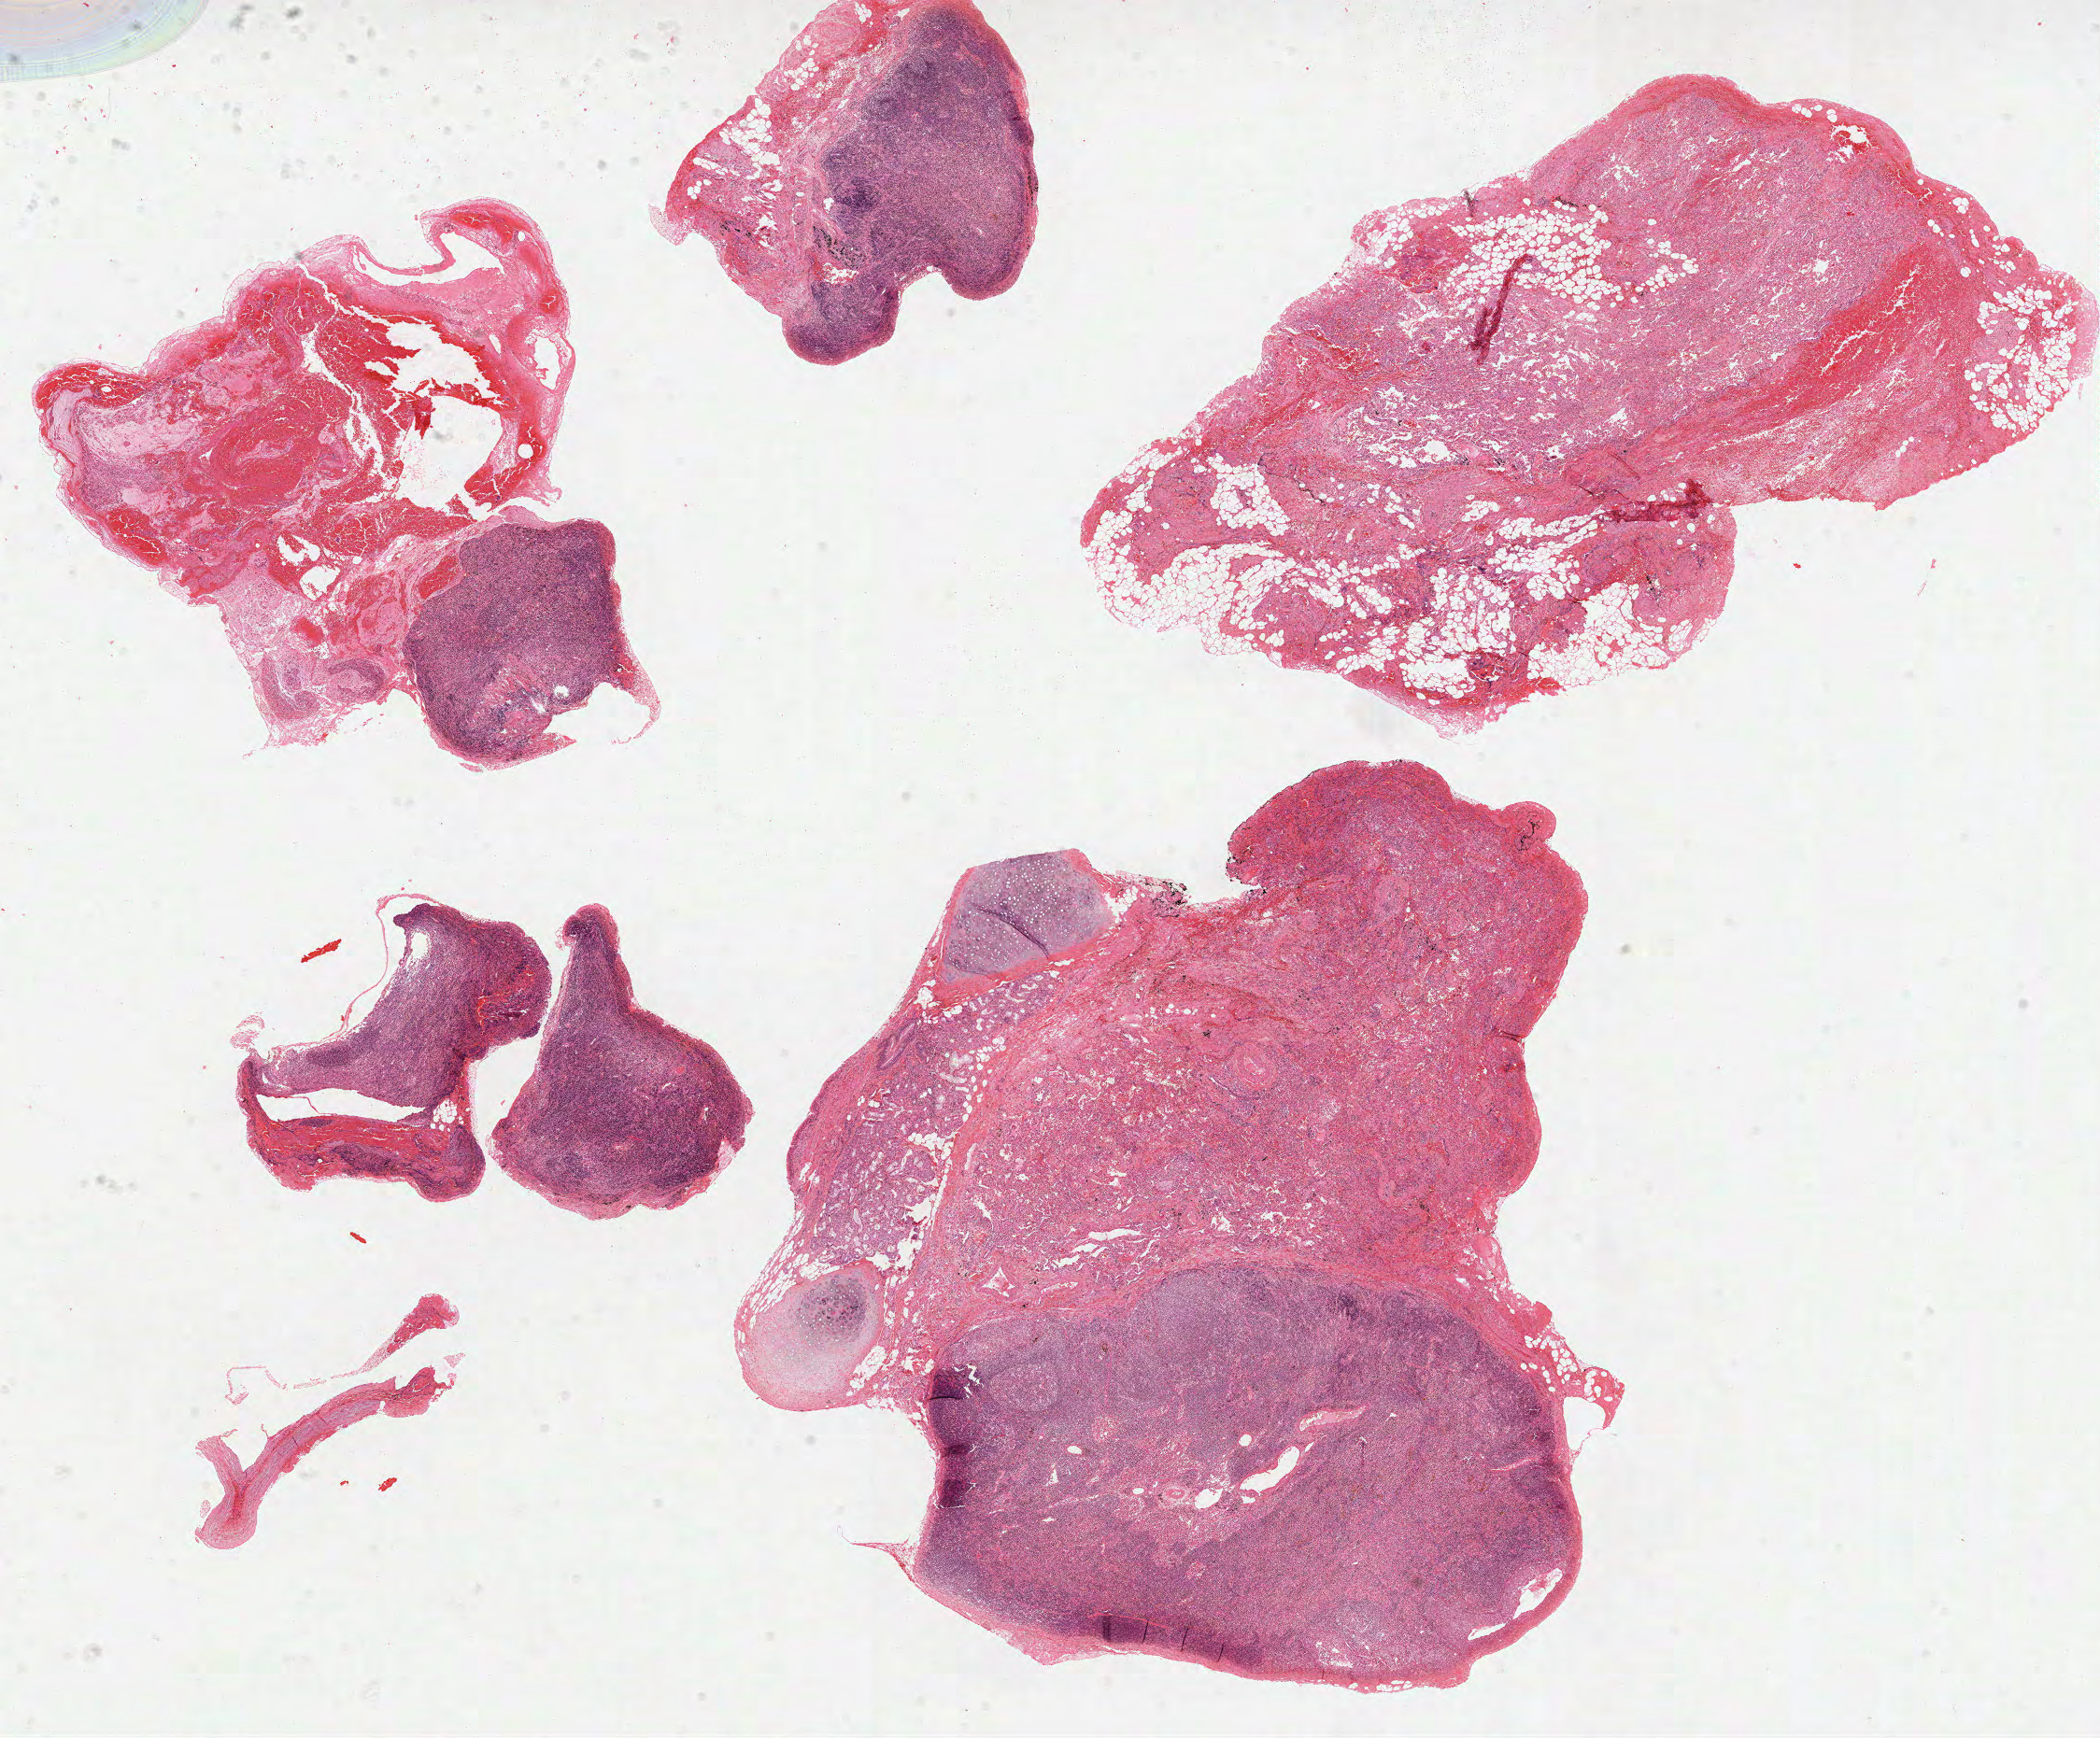
Whole-slide histology image, H&E-stained — whole scanned area (about 18.1 x 15.0 mm, acquisition: 40x scan) shown as a low-resolution overview, FFPE section, primary tumour sample from the lung. Patient: female, age at initial diagnosis 66 years.
AJCC pathologic stage: IIB (6th edition). Histologic diagnosis: Squamous cell carcinoma, NOS.